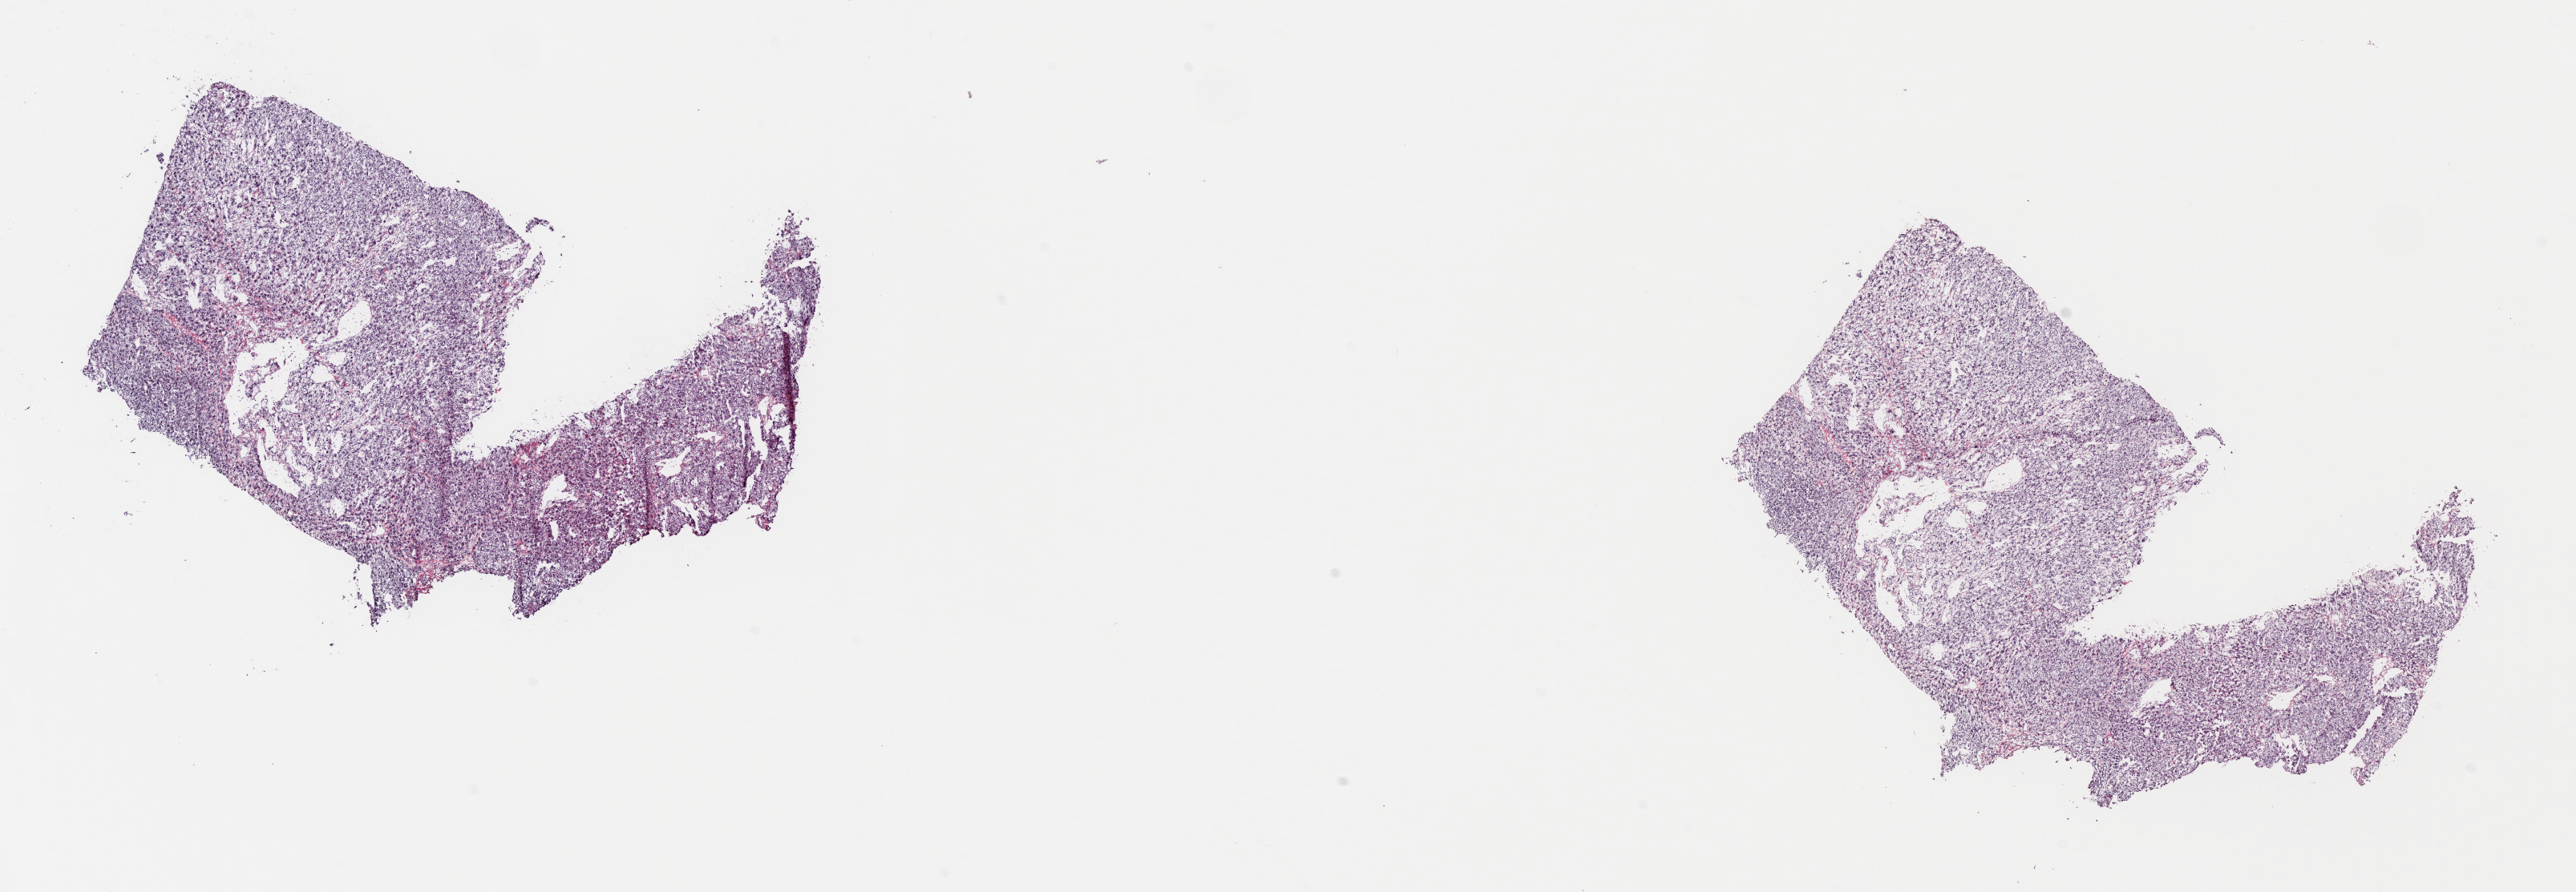
Whole-slide histology image, H&E-stained — whole scanned area (about 25.3 x 8.7 mm, acquisition: 40x scan) shown as a low-resolution overview; frozen section from the top of the tissue portion; primary tumour sample from the liver. Female patient. Pathologist review of this section (percent, as recorded): tumour cells 100%, tumour nuclei 90%, normal cells 0%, stromal cells 0%, necrosis 0%. Inflammatory infiltration, as recorded: lymphocyte infiltration 0%, monocyte infiltration 0%, neutrophil infiltration 0%.
* histologic diagnosis: Hepatocellular carcinoma, clear cell type